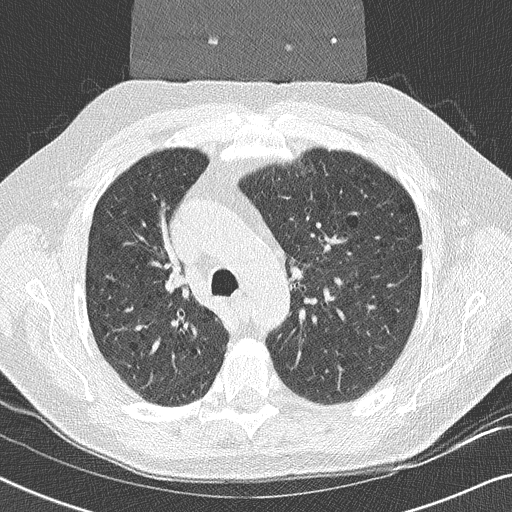
Axial slice from a low-dose chest CT screening exam; second annual screen; lung window (W 1500 / L -600 HU); 2 mm slice thickness; 512 × 512 image matrix, field of view 330 × 330 mm. Male participant, aged 59 years at enrolment. Former smoker at enrolment.
Lesion marked by an expert reader, bounding box <136,254,200,309> (left, top, right, bottom; pixels). Screening reader's record for this exam (one nodule recorded; not confirmed to be the boxed lesion): non-calcified nodule or mass ≥4 mm, right upper lobe, 17 × 16 mm, smooth margins, soft tissue attenuation, pre-existing on the prior screen: yes. Official screen result: positive, other. Later outcome: lung cancer diagnosed 14 days after this screen — squamous cell carcinoma, NOS, right upper lobe, poorly differentiated (G3), stage IIA (AJCC 6th edition), 20 mm at pathology.